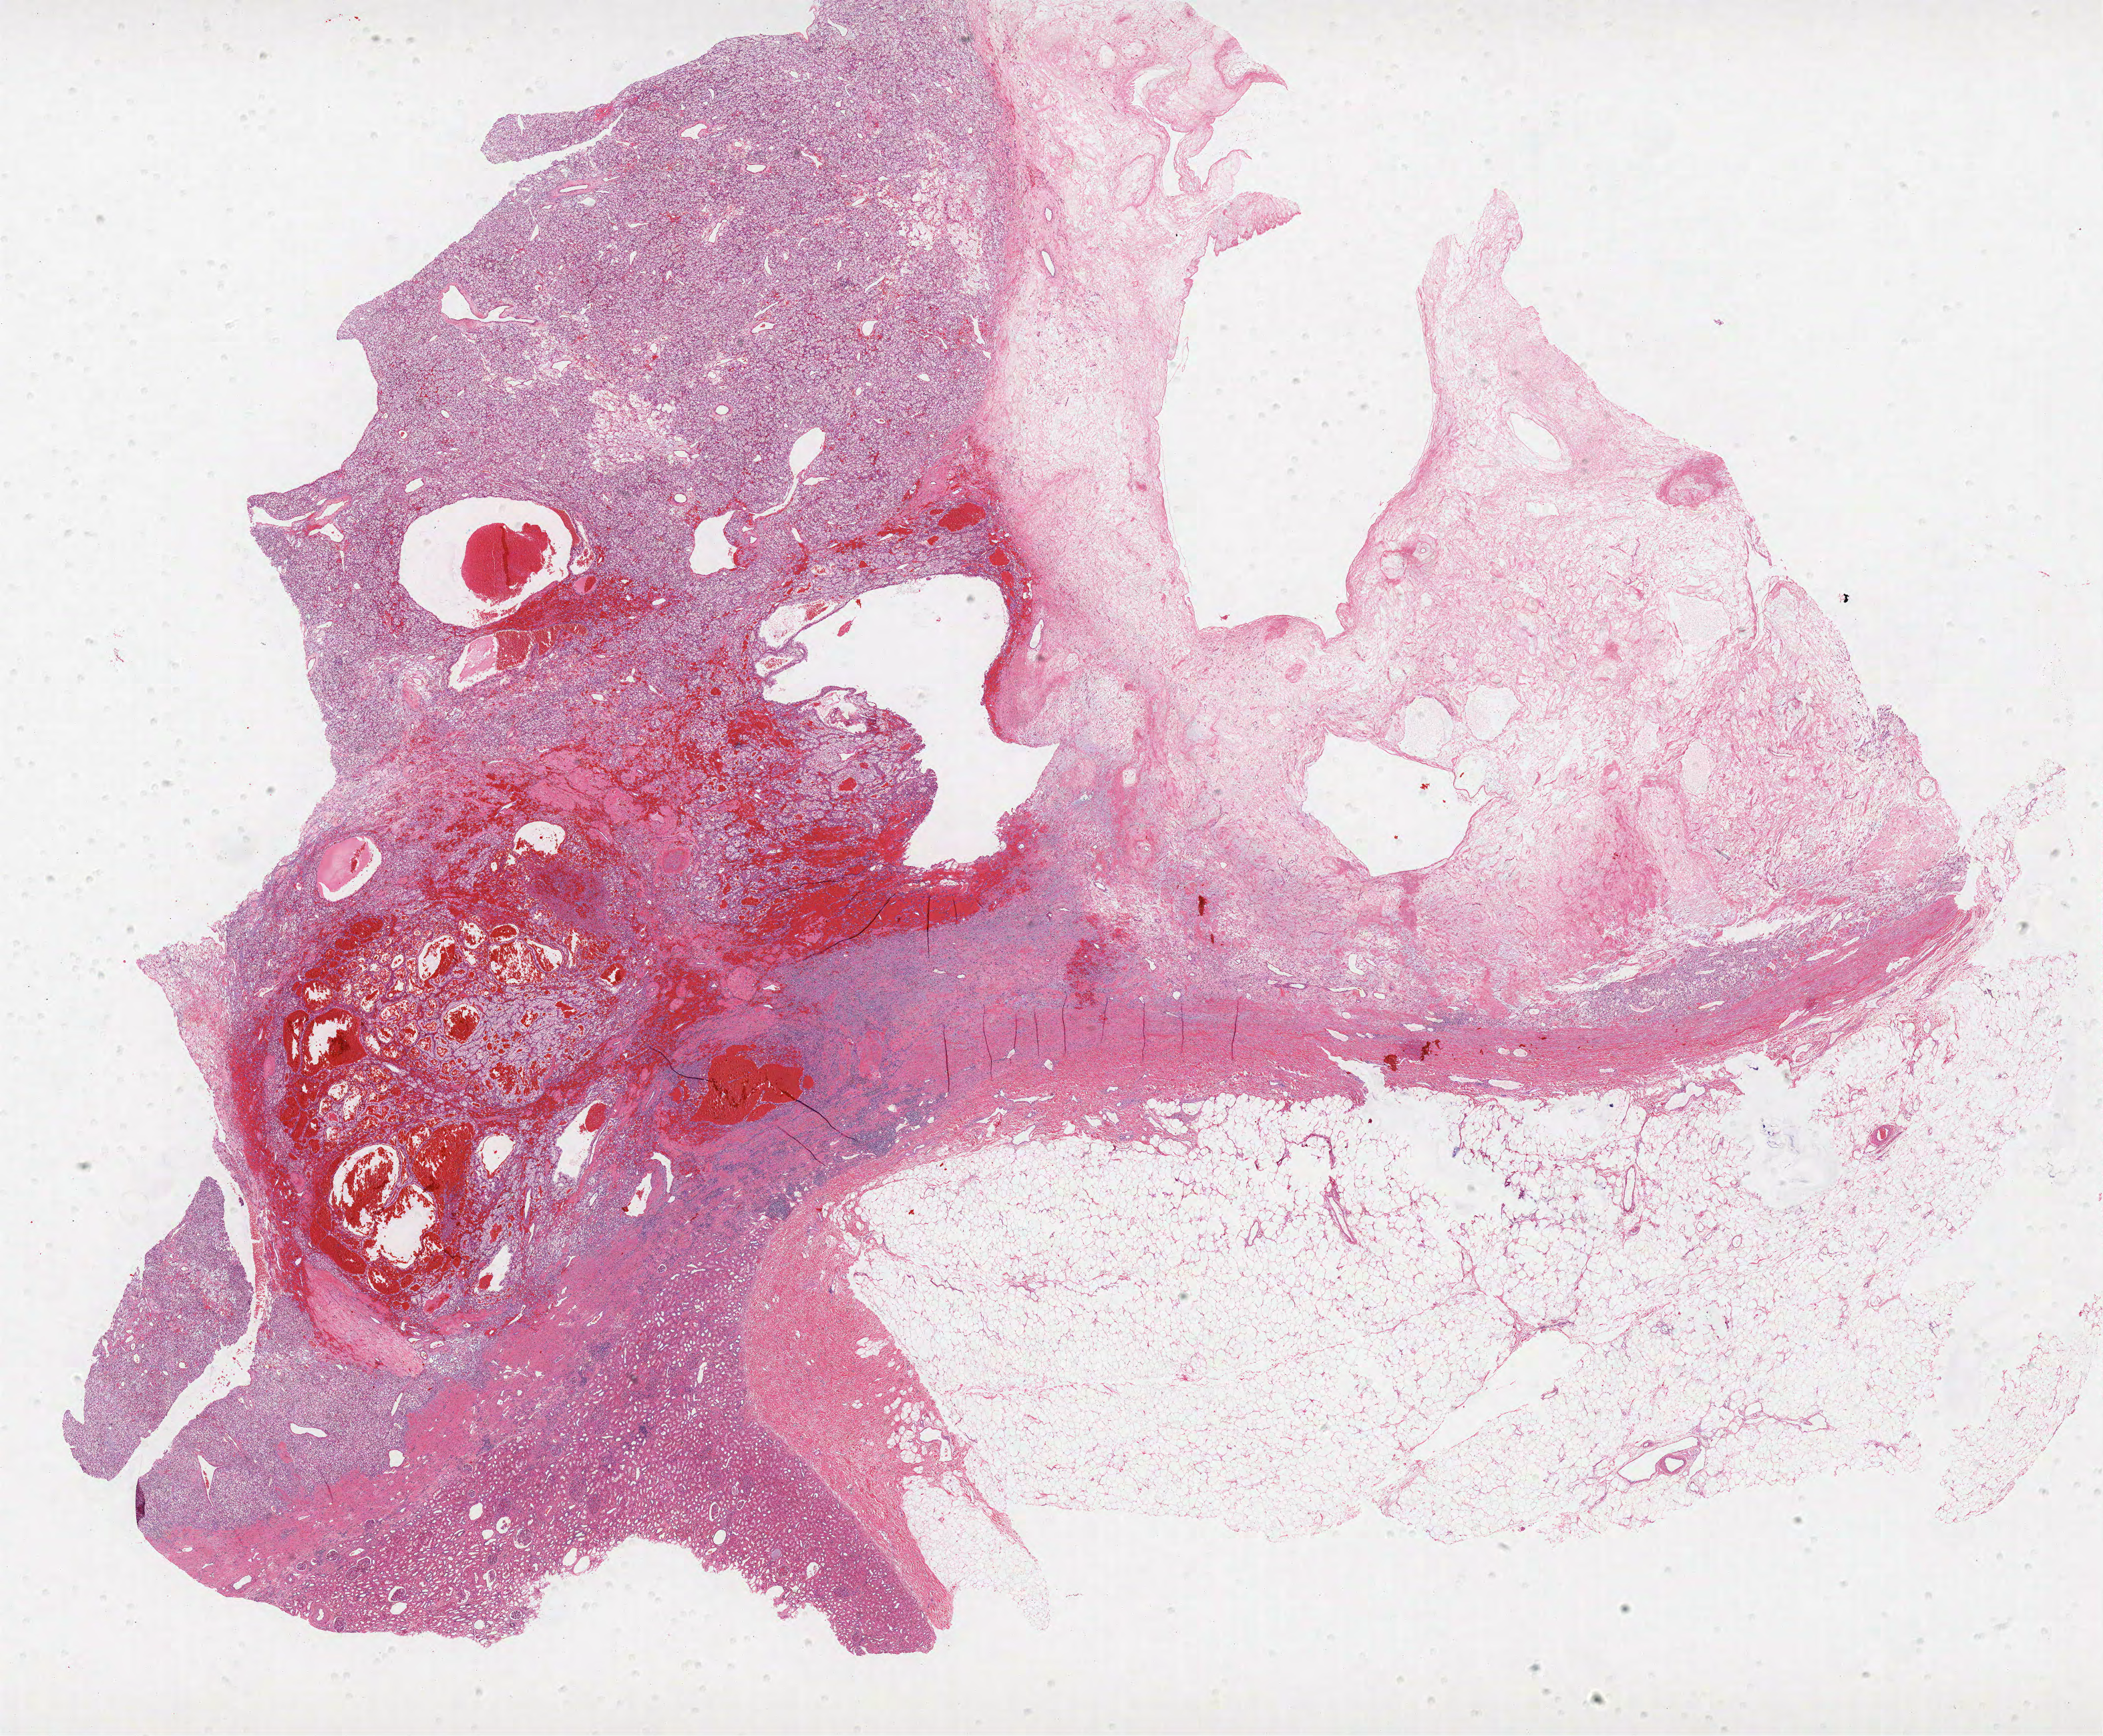
Digitized H&E-stained tissue section (whole slide), a low-resolution overview of the entire scanned area, about 25.2 x 20.8 mm. FFPE section. Sample: primary tumour, kidney. Male patient; age at initial diagnosis 56 years.
Pathologic diagnosis: Clear cell adenocarcinoma, NOS.